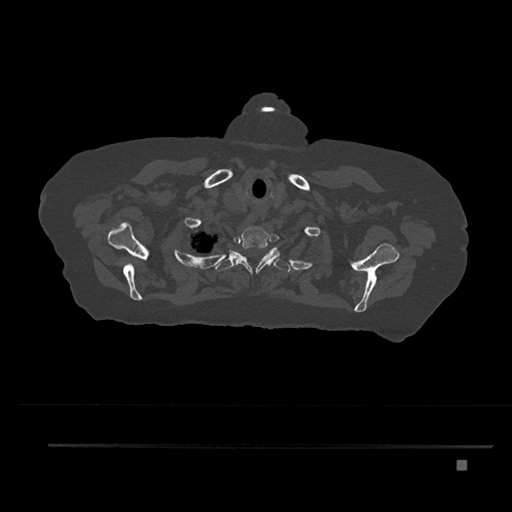
CT including the spine, one axial slice; slice 686 of 797 in the series (ordered by position); reconstruction kernel Br40s/3; 120 kVp; bone window (W 1800 / L 400 HU); 0.5 mm slice thickness; 512 × 512 image matrix, field of view 437 × 437 mm. Patient: female, 76 years. From the clinical record (not read from this slice): primary cancer: lung; vertebrae with lytic lesions (as recorded): T11, L3.
Structures marked on this image (semi-automatically segmented with operator editing):
- T1 vertebra: bounding box <234,227,280,274> (left, top, right, bottom; pixels)
- T2 vertebra: <207,247,290,272>